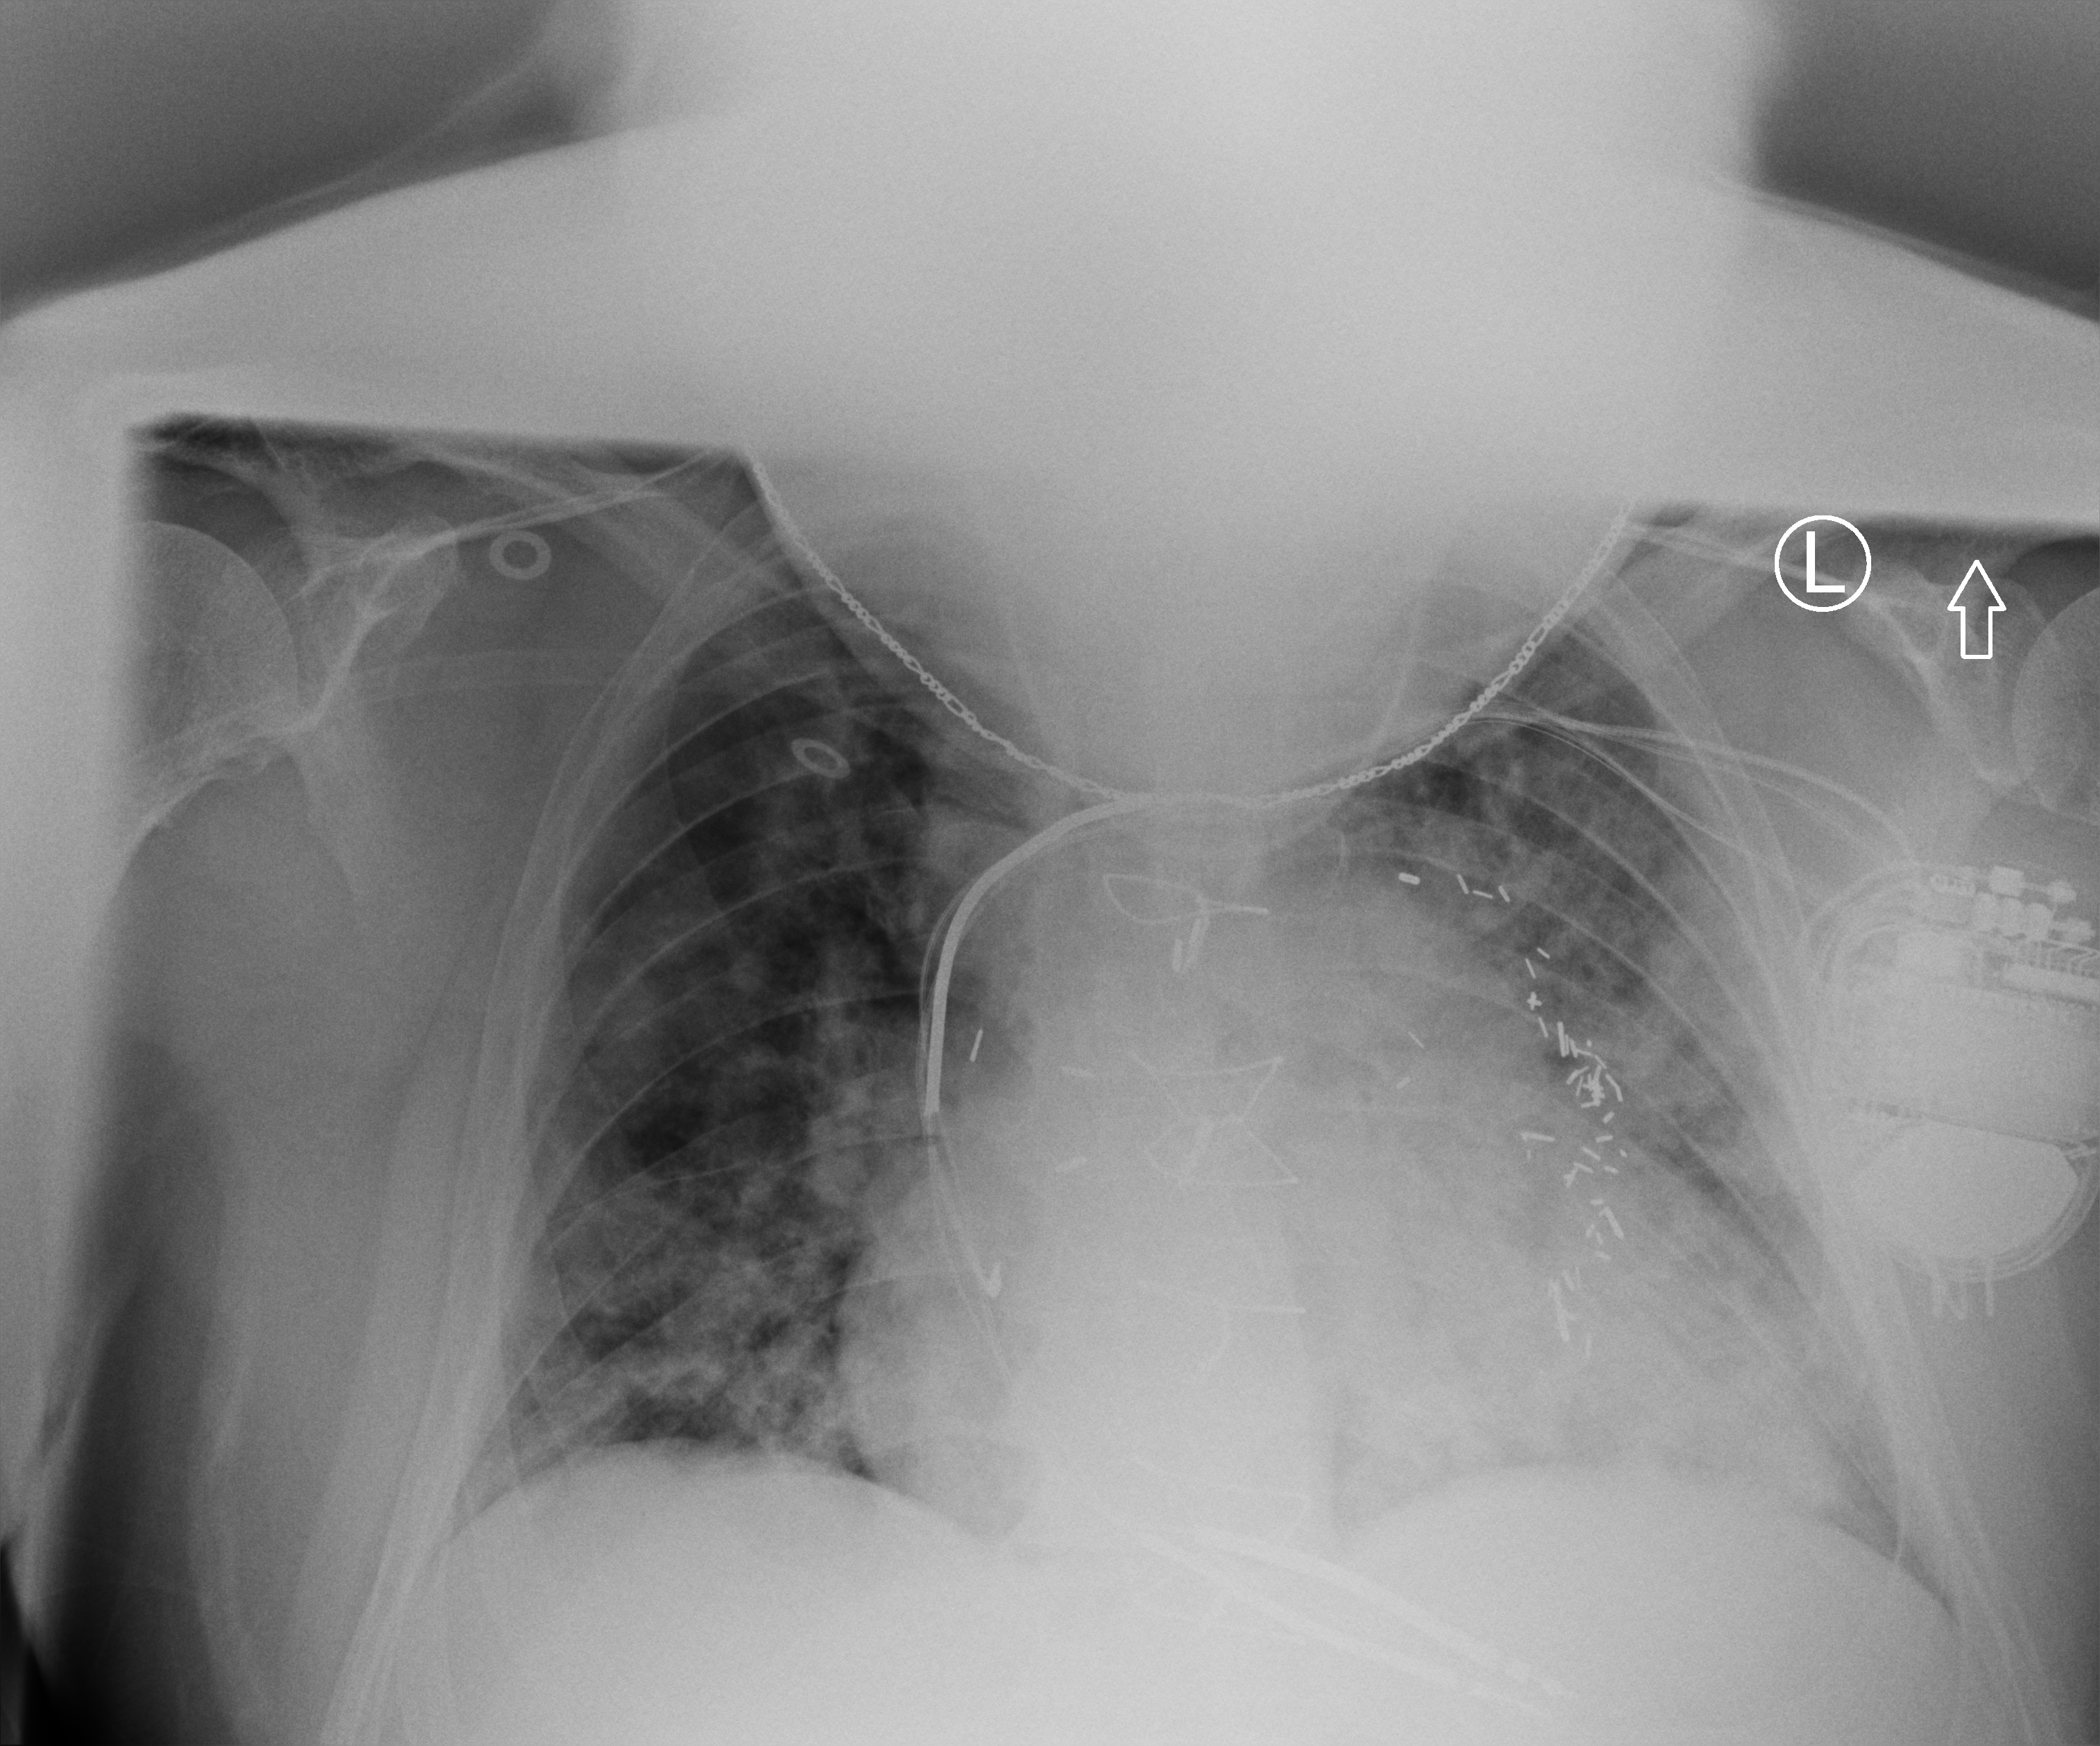
Bedside chest radiograph (computed radiography), anteroposterior (AP) projection. Male patient hospitalised with COVID-19, age 60–74 years.
From the hospital-stay record, not from the radiograph (when in the stay this image was taken is not recorded):
- length of hospital stay: 55 days
- mechanically ventilated during this hospital stay: yes
- admitted to intensive care during this hospital stay: yes